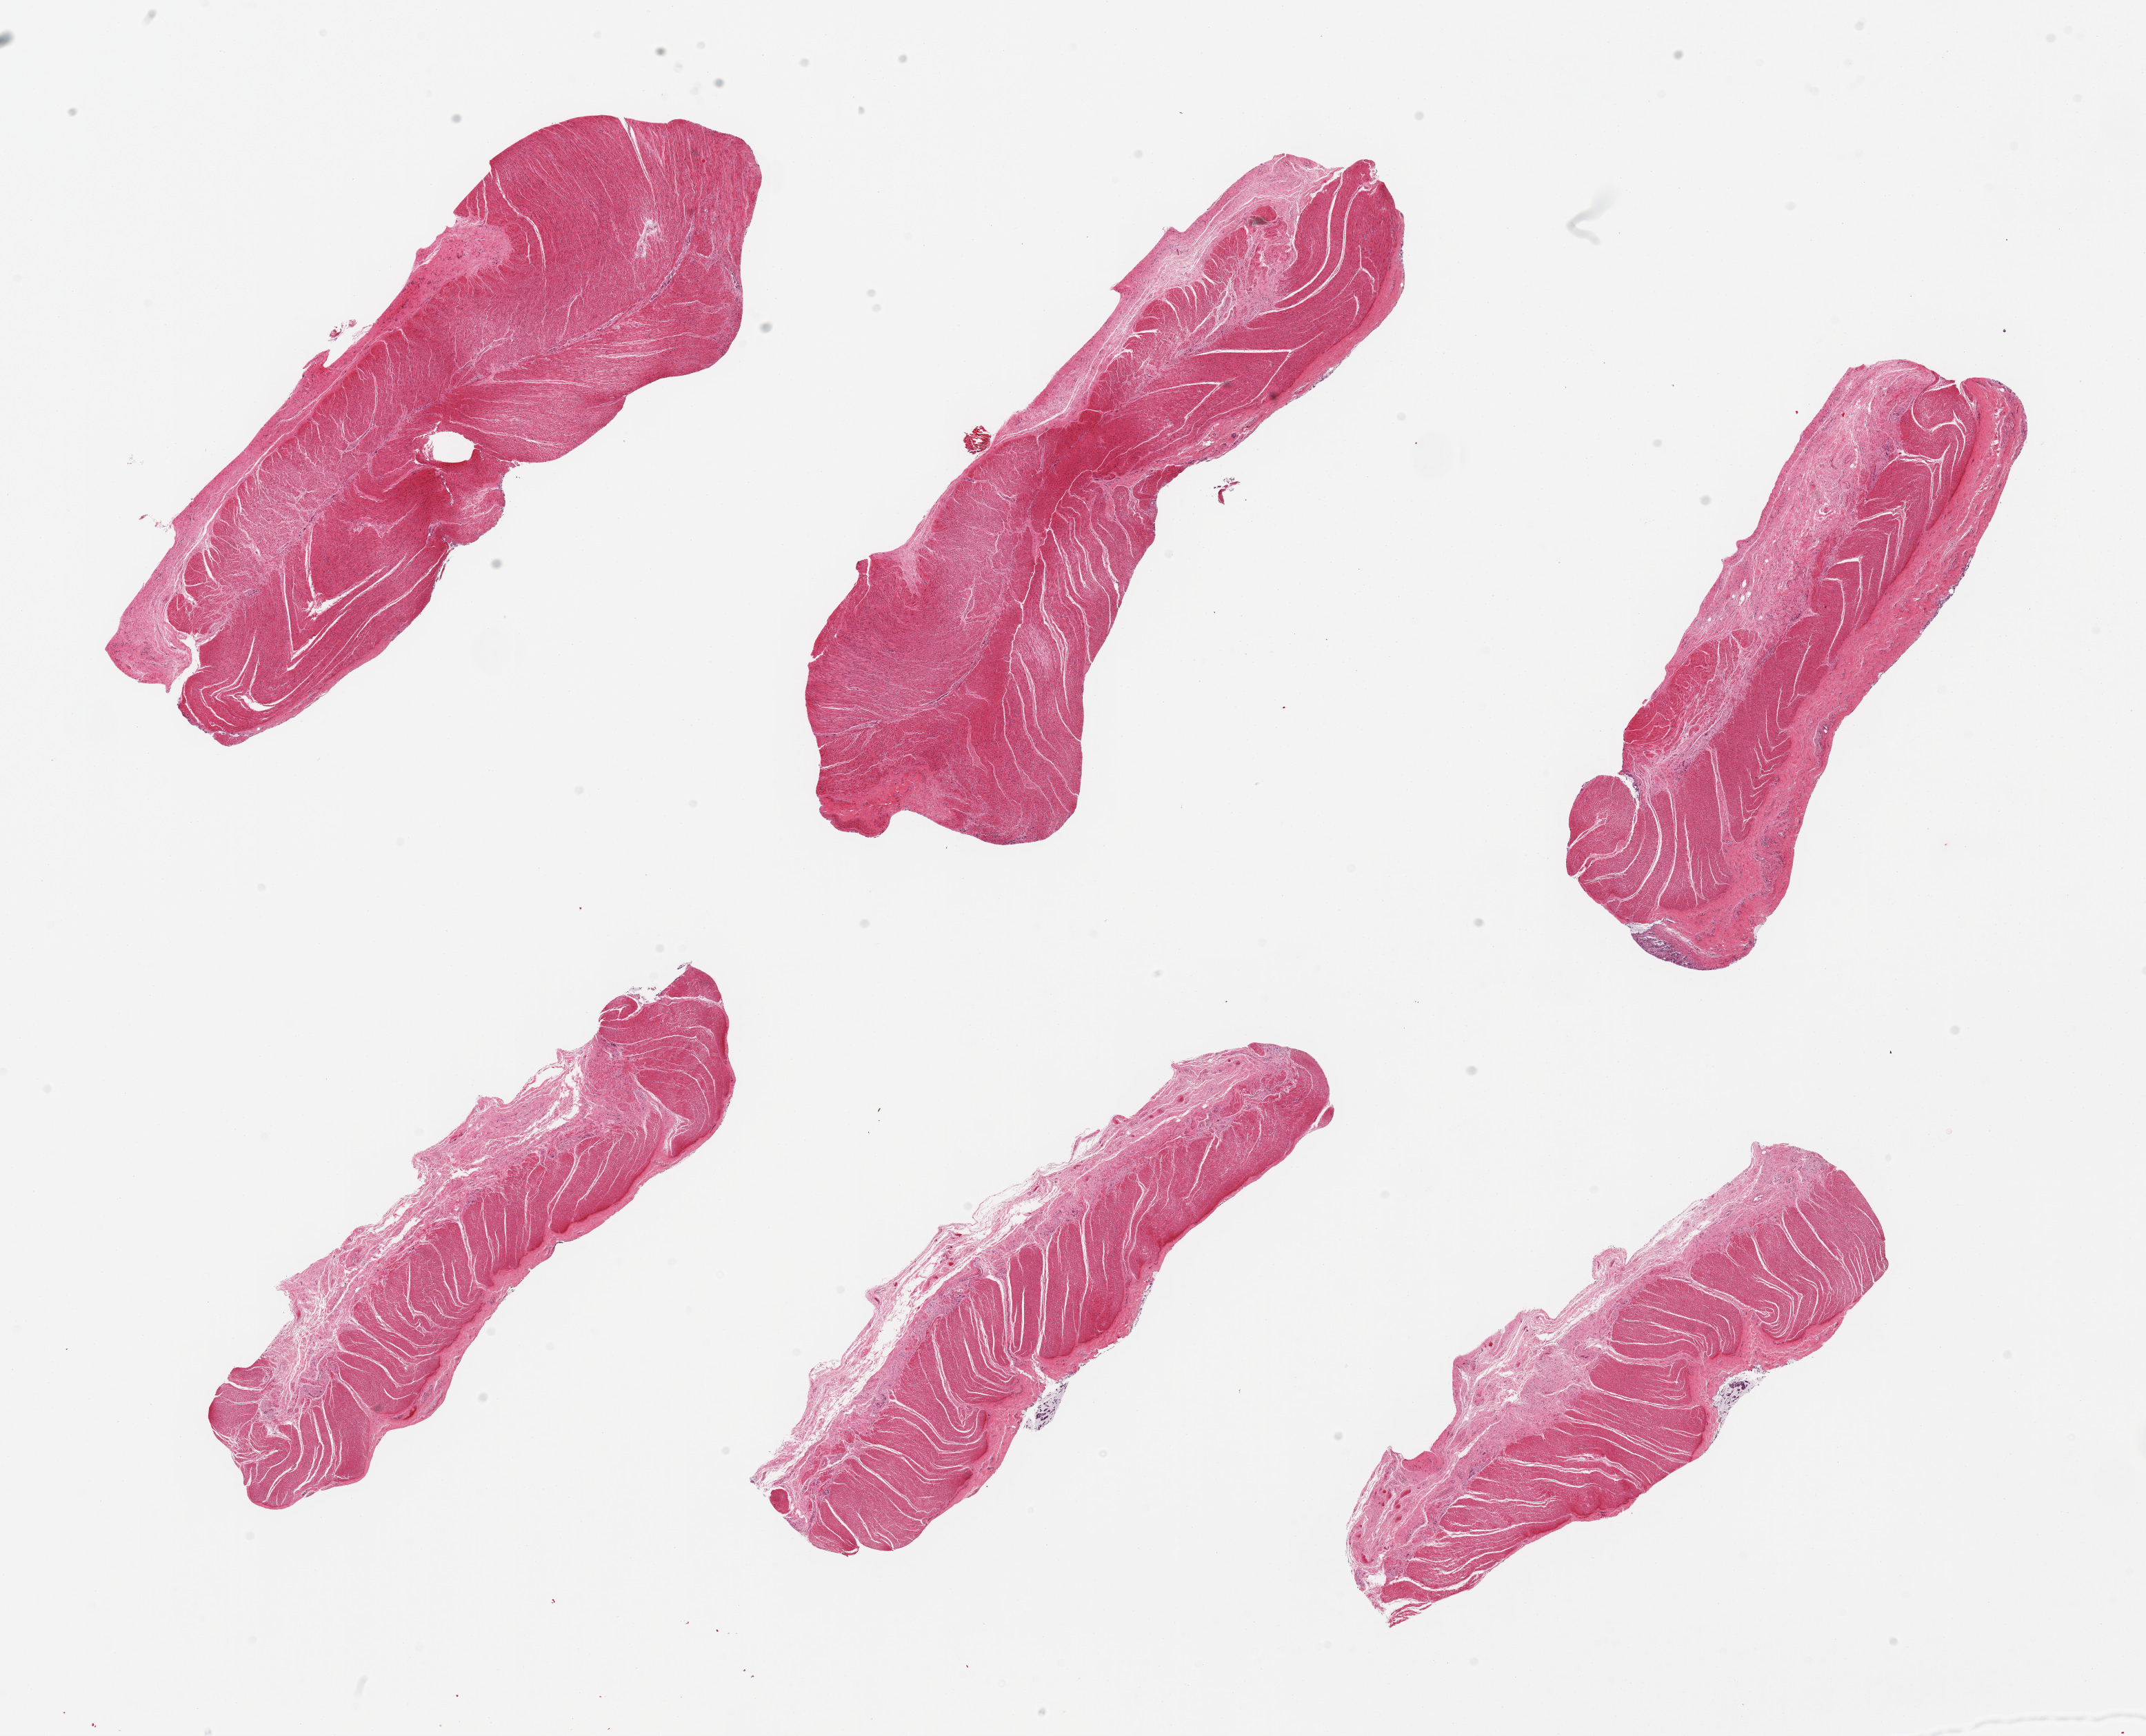
Whole-slide image, H&E stain, brightfield, shown as a low-resolution overview of the whole scanned area (about 24.6 x 19.9 mm, acquisition: 20x scan), PAXgene-fixed, paraffin-embedded tissue, section of sigmoid colon (target tissue), tissue donor sample. Donor: male.
- review note (as recorded): 6 pieces, mildly edematous, all target muscularis, good specimens